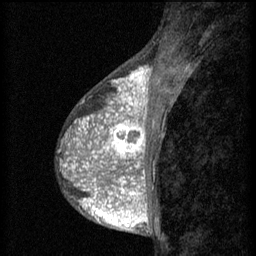
Breast MRI (dynamic contrast-enhanced), one sagittal slice. Position 25 of 60 along the scan axis. 3 images stored at this slice position (order not interpretable as contrast timing). 1.5 T. TE 4.2 ms, TR 8.2 ms. 2 mm slice thickness. 256 × 256 image matrix, field of view 180 × 180 mm. Female patient, age 38 years.
Annotated regions visible in this slice (semi-automatically segmented with operator editing):
- analysis volume of interest (the breast-tissue region the enhancement analysis was run in; not a lesion): bounding box (x1, y1, x2, y2) in pixels: (92, 112, 152, 171)
- tumour enhancement mask (voxels above the 70 % enhancement threshold inside the analysis volume of interest): (92, 112, 147, 171)